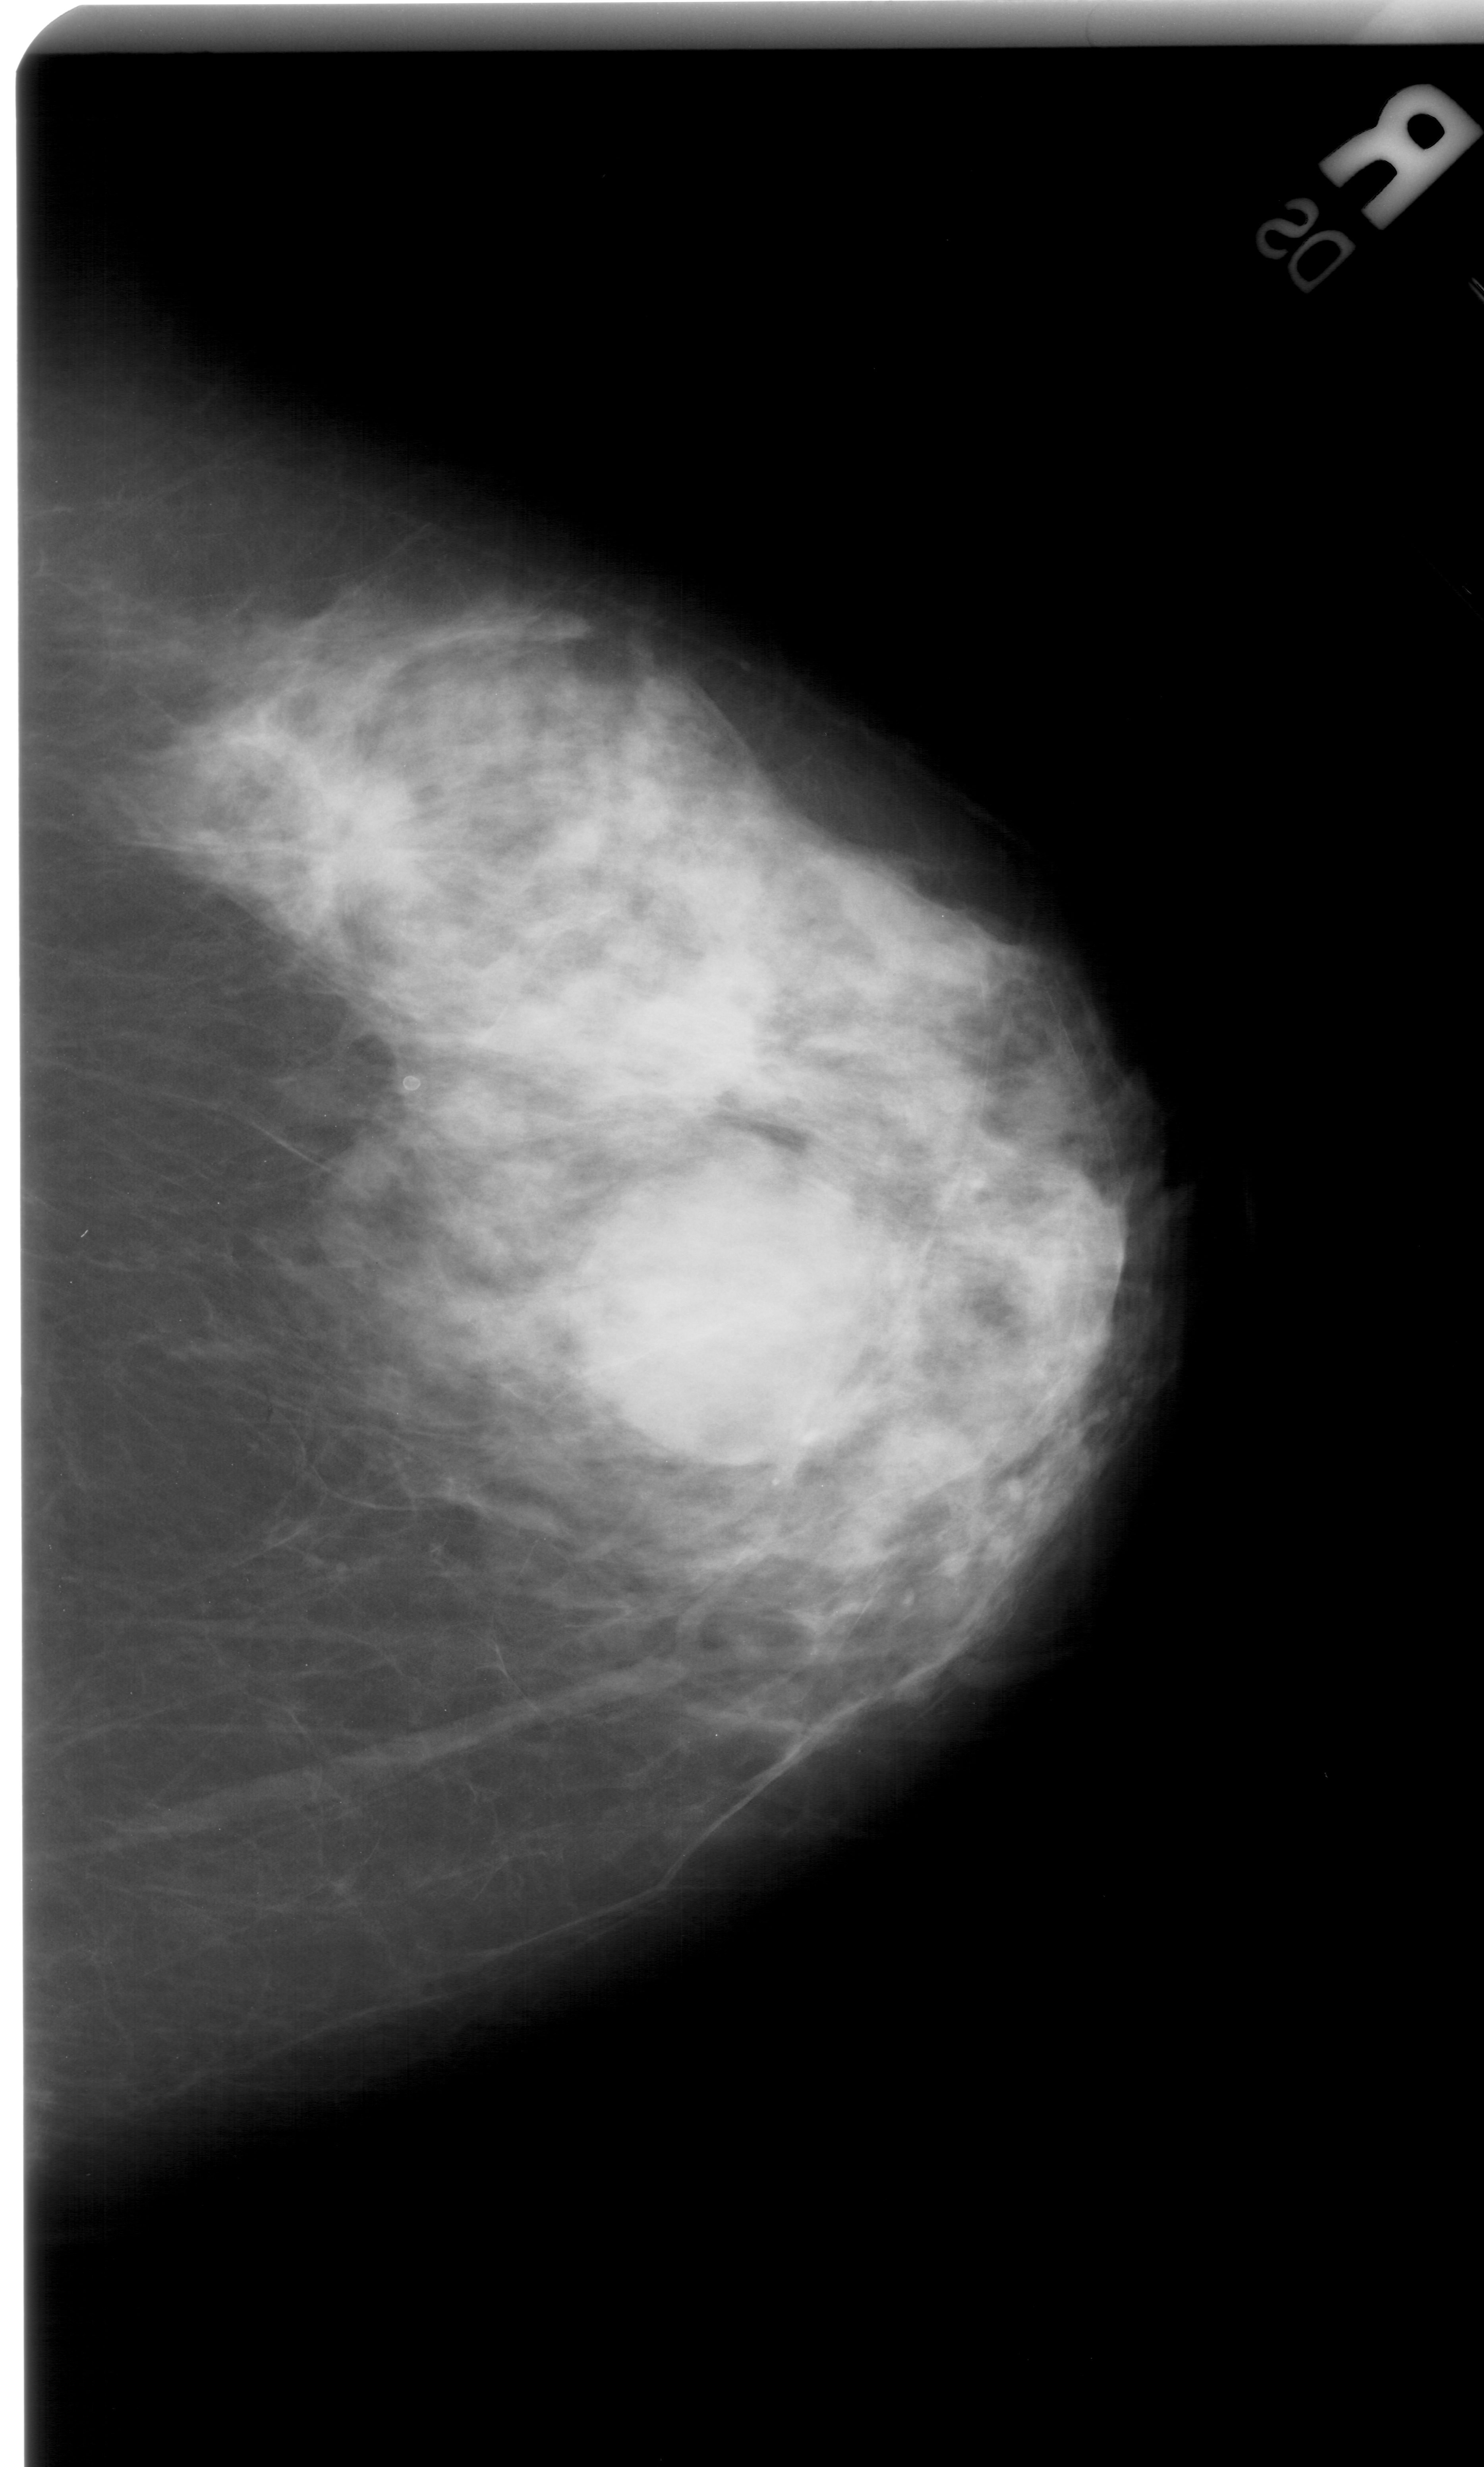
Mammogram (digitized film); right breast; CC view; breast composition: extremely dense (BI-RADS density category 4 of 4).
Marked findings (only marked abnormalities are described; nothing is implied about the rest of the image): mass, shape irregular, margins spiculated; BI-RADS assessment category 5; subtlety rating 4 on a 1 (subtle) to 5 (obvious) scale; pathology (as recorded): malignant.